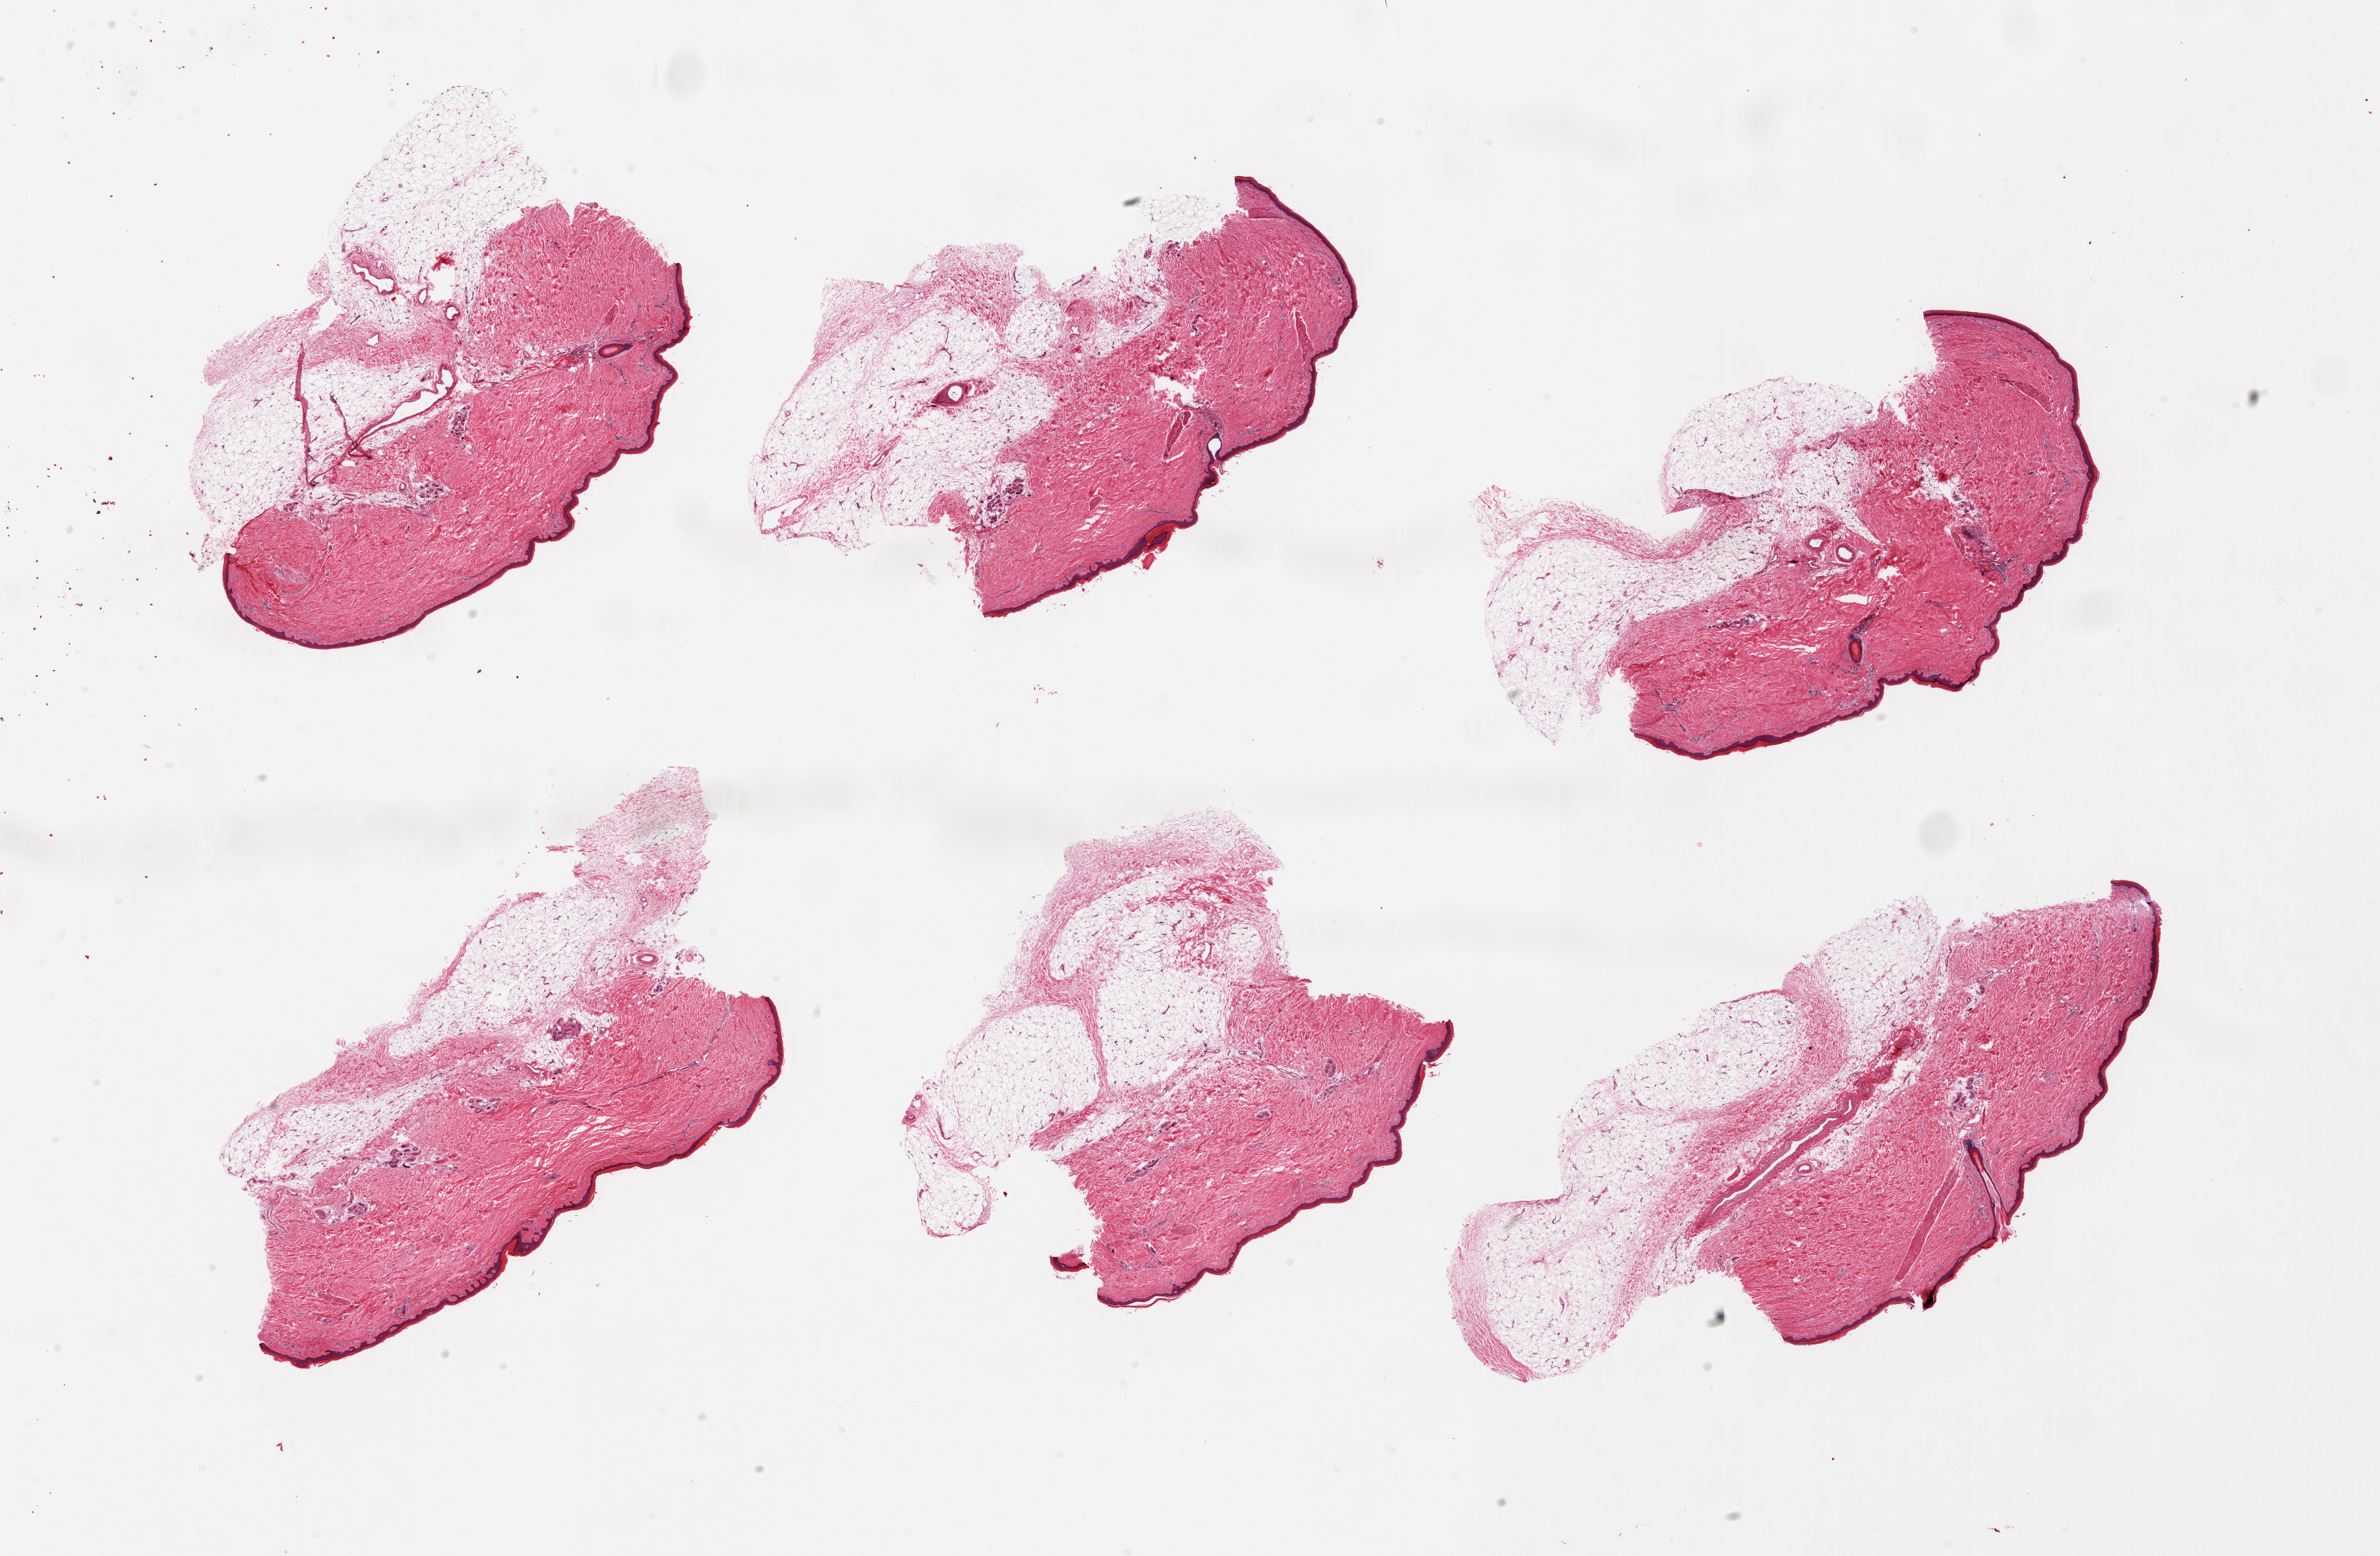
Digitized H&E-stained section, whole scanned area (about 28.5 x 18.7 mm, acquisition: 20x scan) shown as a low-resolution overview. PAXgene-fixed, paraffin-embedded tissue. Section of skin of lower leg (target tissue). Tissue donor sample. Donor sex: male.
• pathologist's review note for this sample: 6 pieces; thin epidermis up to ~30 micron thick; ~50% external fat